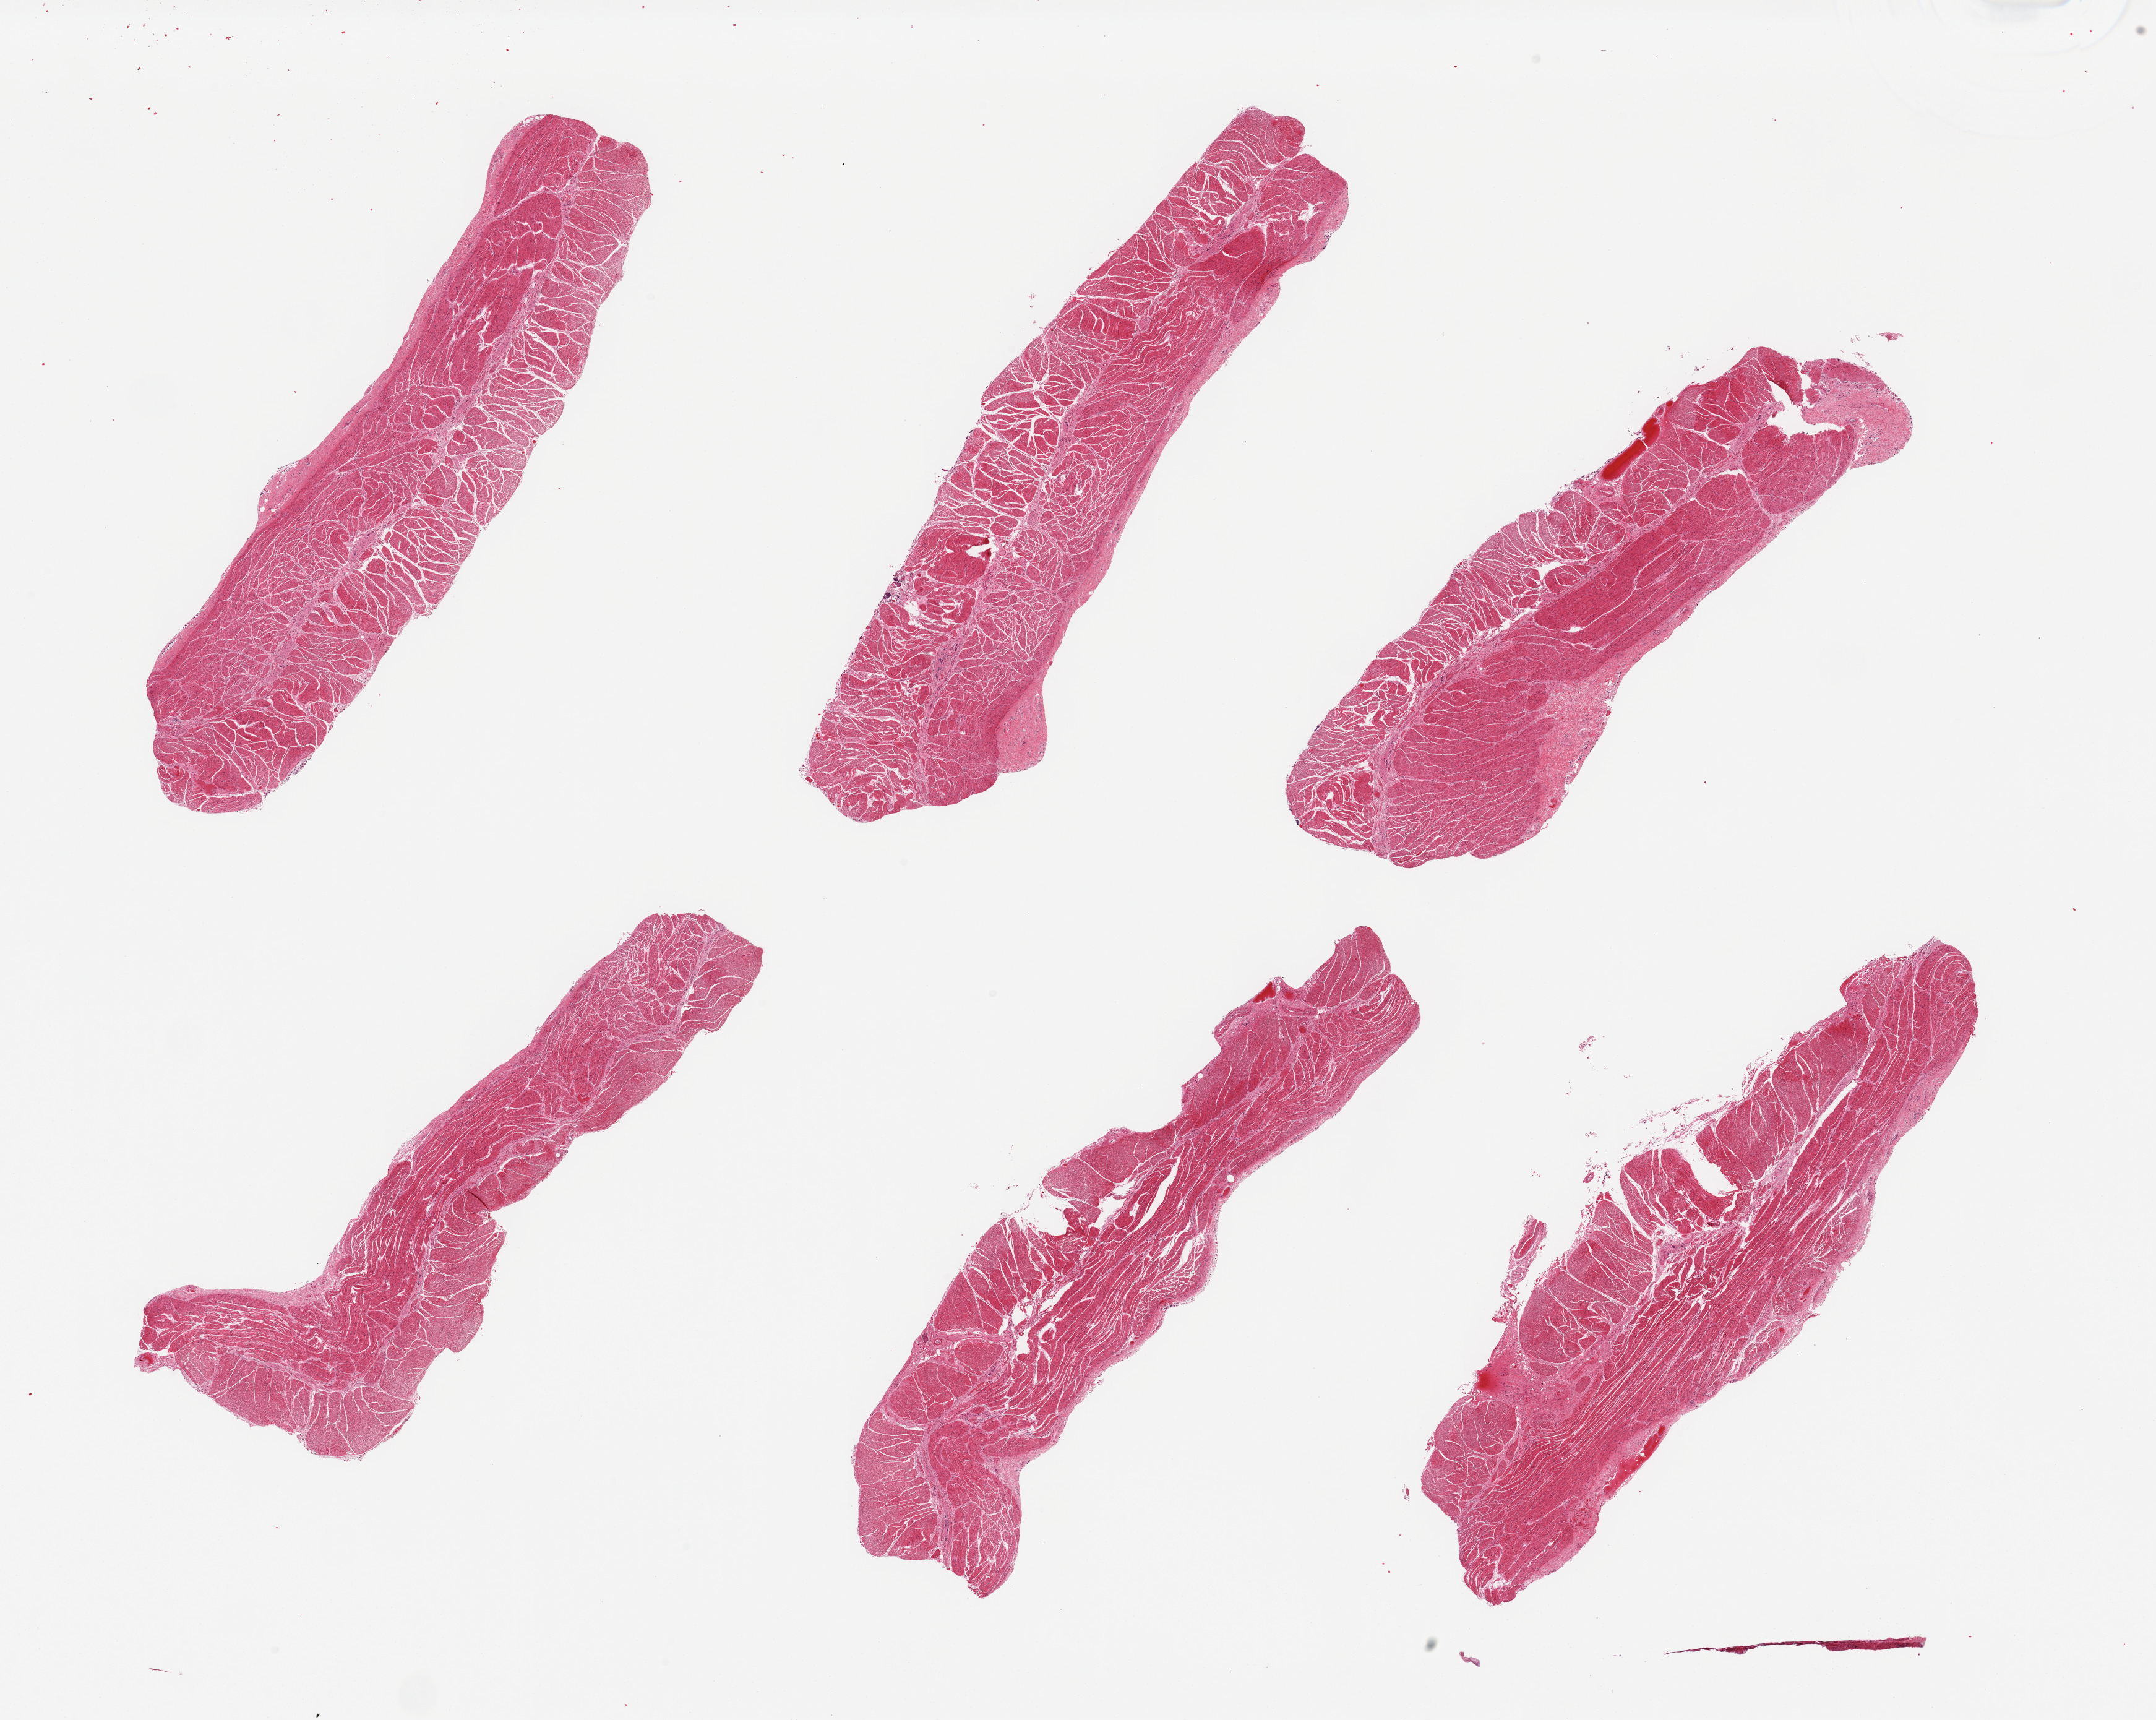
Haematoxylin and eosin whole-slide image, a low-resolution overview of the entire scanned area, about 27.6 x 22.0 mm; PAXgene-fixed, paraffin-embedded tissue; target tissue: esophageal muscle; tissue donor sample.
* pathologist's review note for this sample: 6 pieces, confirmed target muscularis